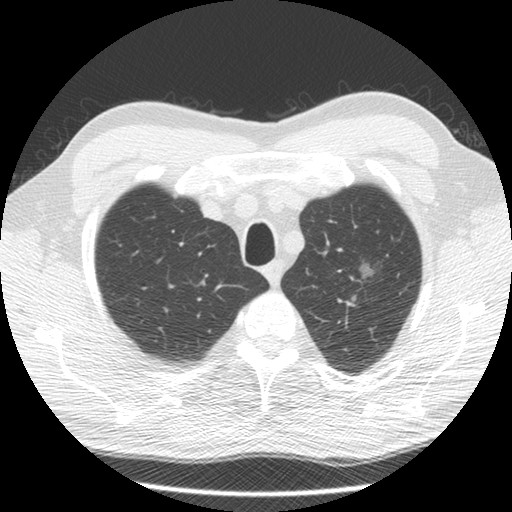
Low-dose screening chest CT, one axial slice. Position 113 of 132 along the scan axis. Lung window (W 1500 / L -600 HU). 2.5 mm slice thickness. 512 × 512 image matrix.
Outlined on this slice (expert manual segmentation):
- lesion 1 (tumor, upper lobe of left lung): box from (x=357, y=264) to (x=373, y=282) px